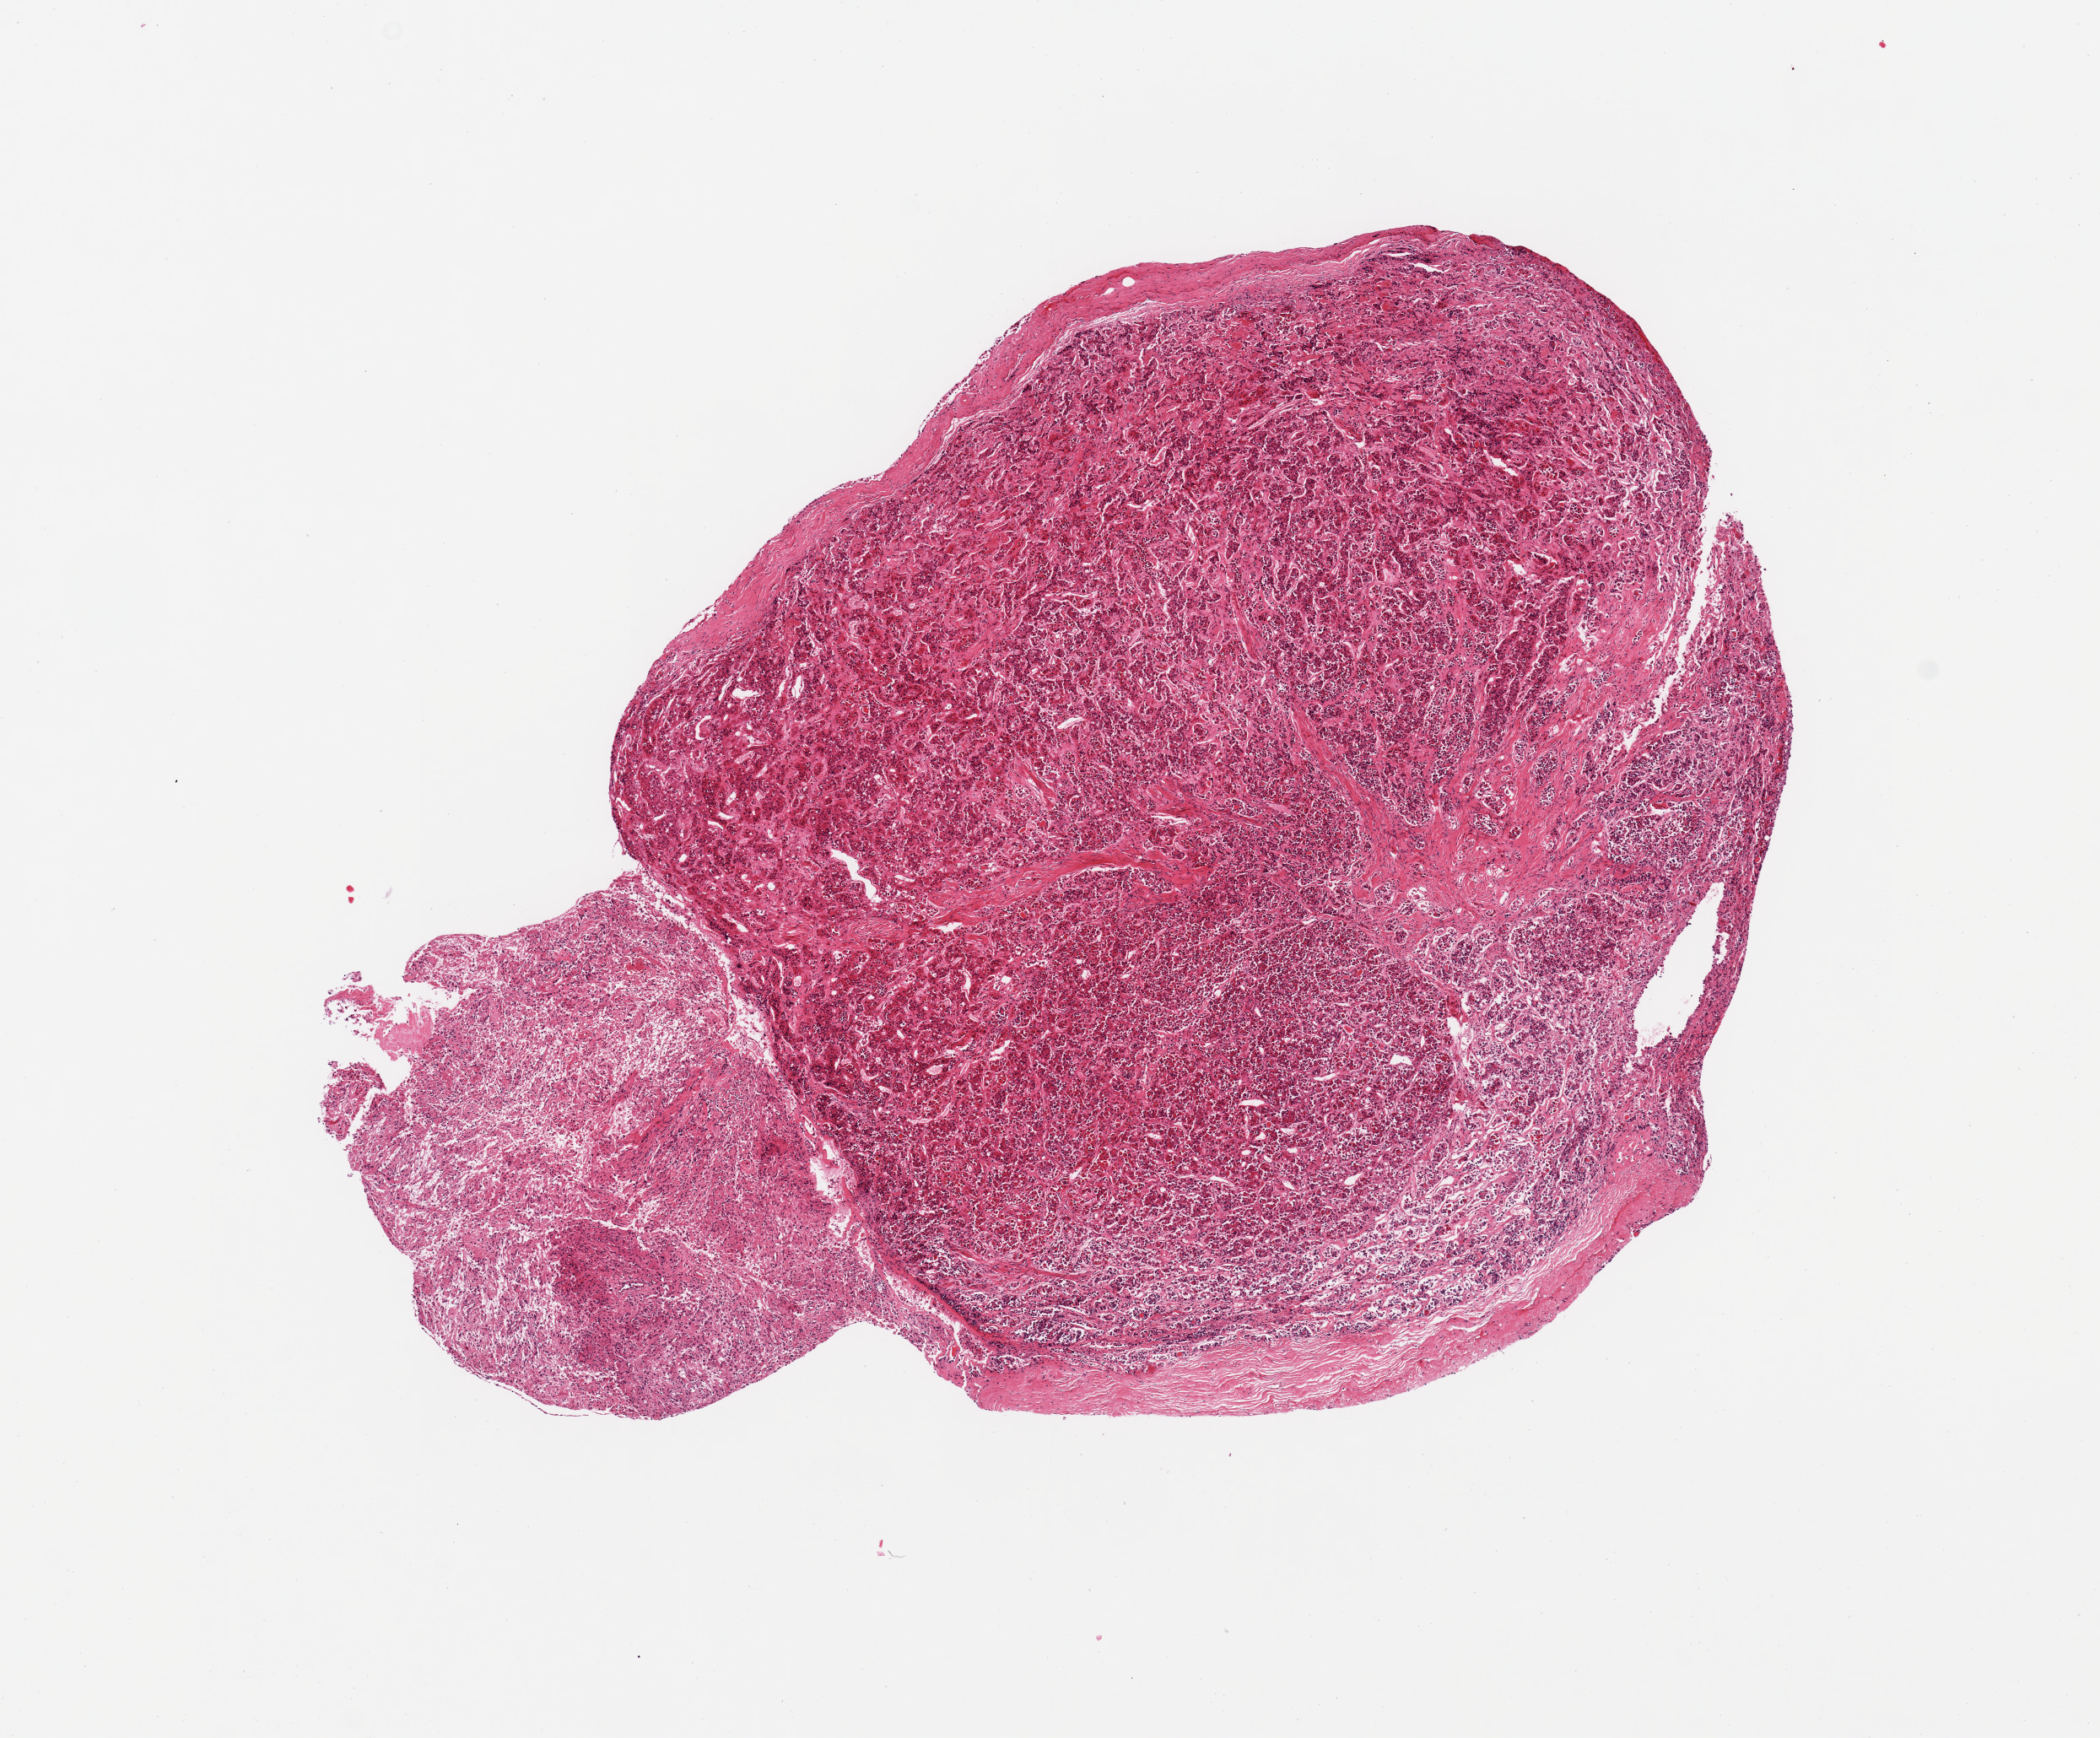
Hematoxylin and eosin (H&E) whole-slide image, brightfield, a low-resolution overview of the entire scanned area, about 9.8 x 8.1 mm (slide scanned at 20x); PAXgene-fixed paraffin-embedded (PFPE) section; target tissue: pituitary; donor tissue sample.
Pathologist's review note for this sample: 1 piece; neurohypophysis comprises 20%.